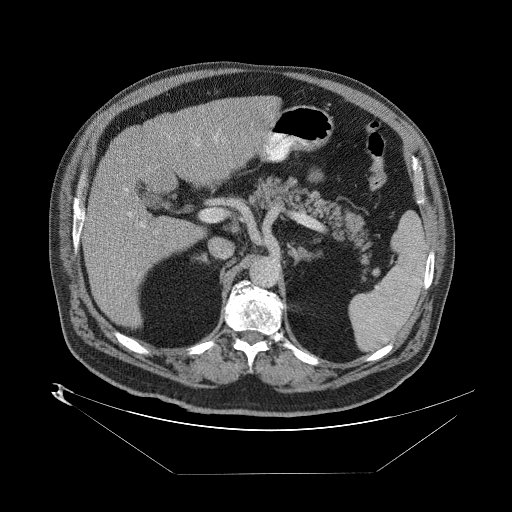
Contrast-enhanced abdominal CT (liver protocol), one axial slice; position 41 of 89 along the scan axis; reconstruction kernel STANDARD; one of 2 acquisitions stored at this slice position; soft-tissue window (W 400 / L 40 HU); 2.5 mm slice thickness; 512 × 512 image matrix, field of view 480 × 480 mm. From the clinical record (not read from this slice): diagnosis: hepatocellular carcinoma (patient treated with transarterial chemoembolisation; whether this scan precedes or follows treatment is not stated here); TNM stage (as recorded): Stage-II; Child-Pugh class: B; tumour differentiation: moderately differentiated; tumour size: 4 cm.
Structures marked on this image (semi-automatically segmented with operator editing):
- abdominal aorta: bounding box (x1, y1, x2, y2) in pixels: (250, 258, 277, 285)
- liver parenchyma outside the tumour (the mass and vessels are separate outlines, so this box may not span the whole liver): (82, 94, 276, 332)
- liver vessels: (98, 136, 224, 273)